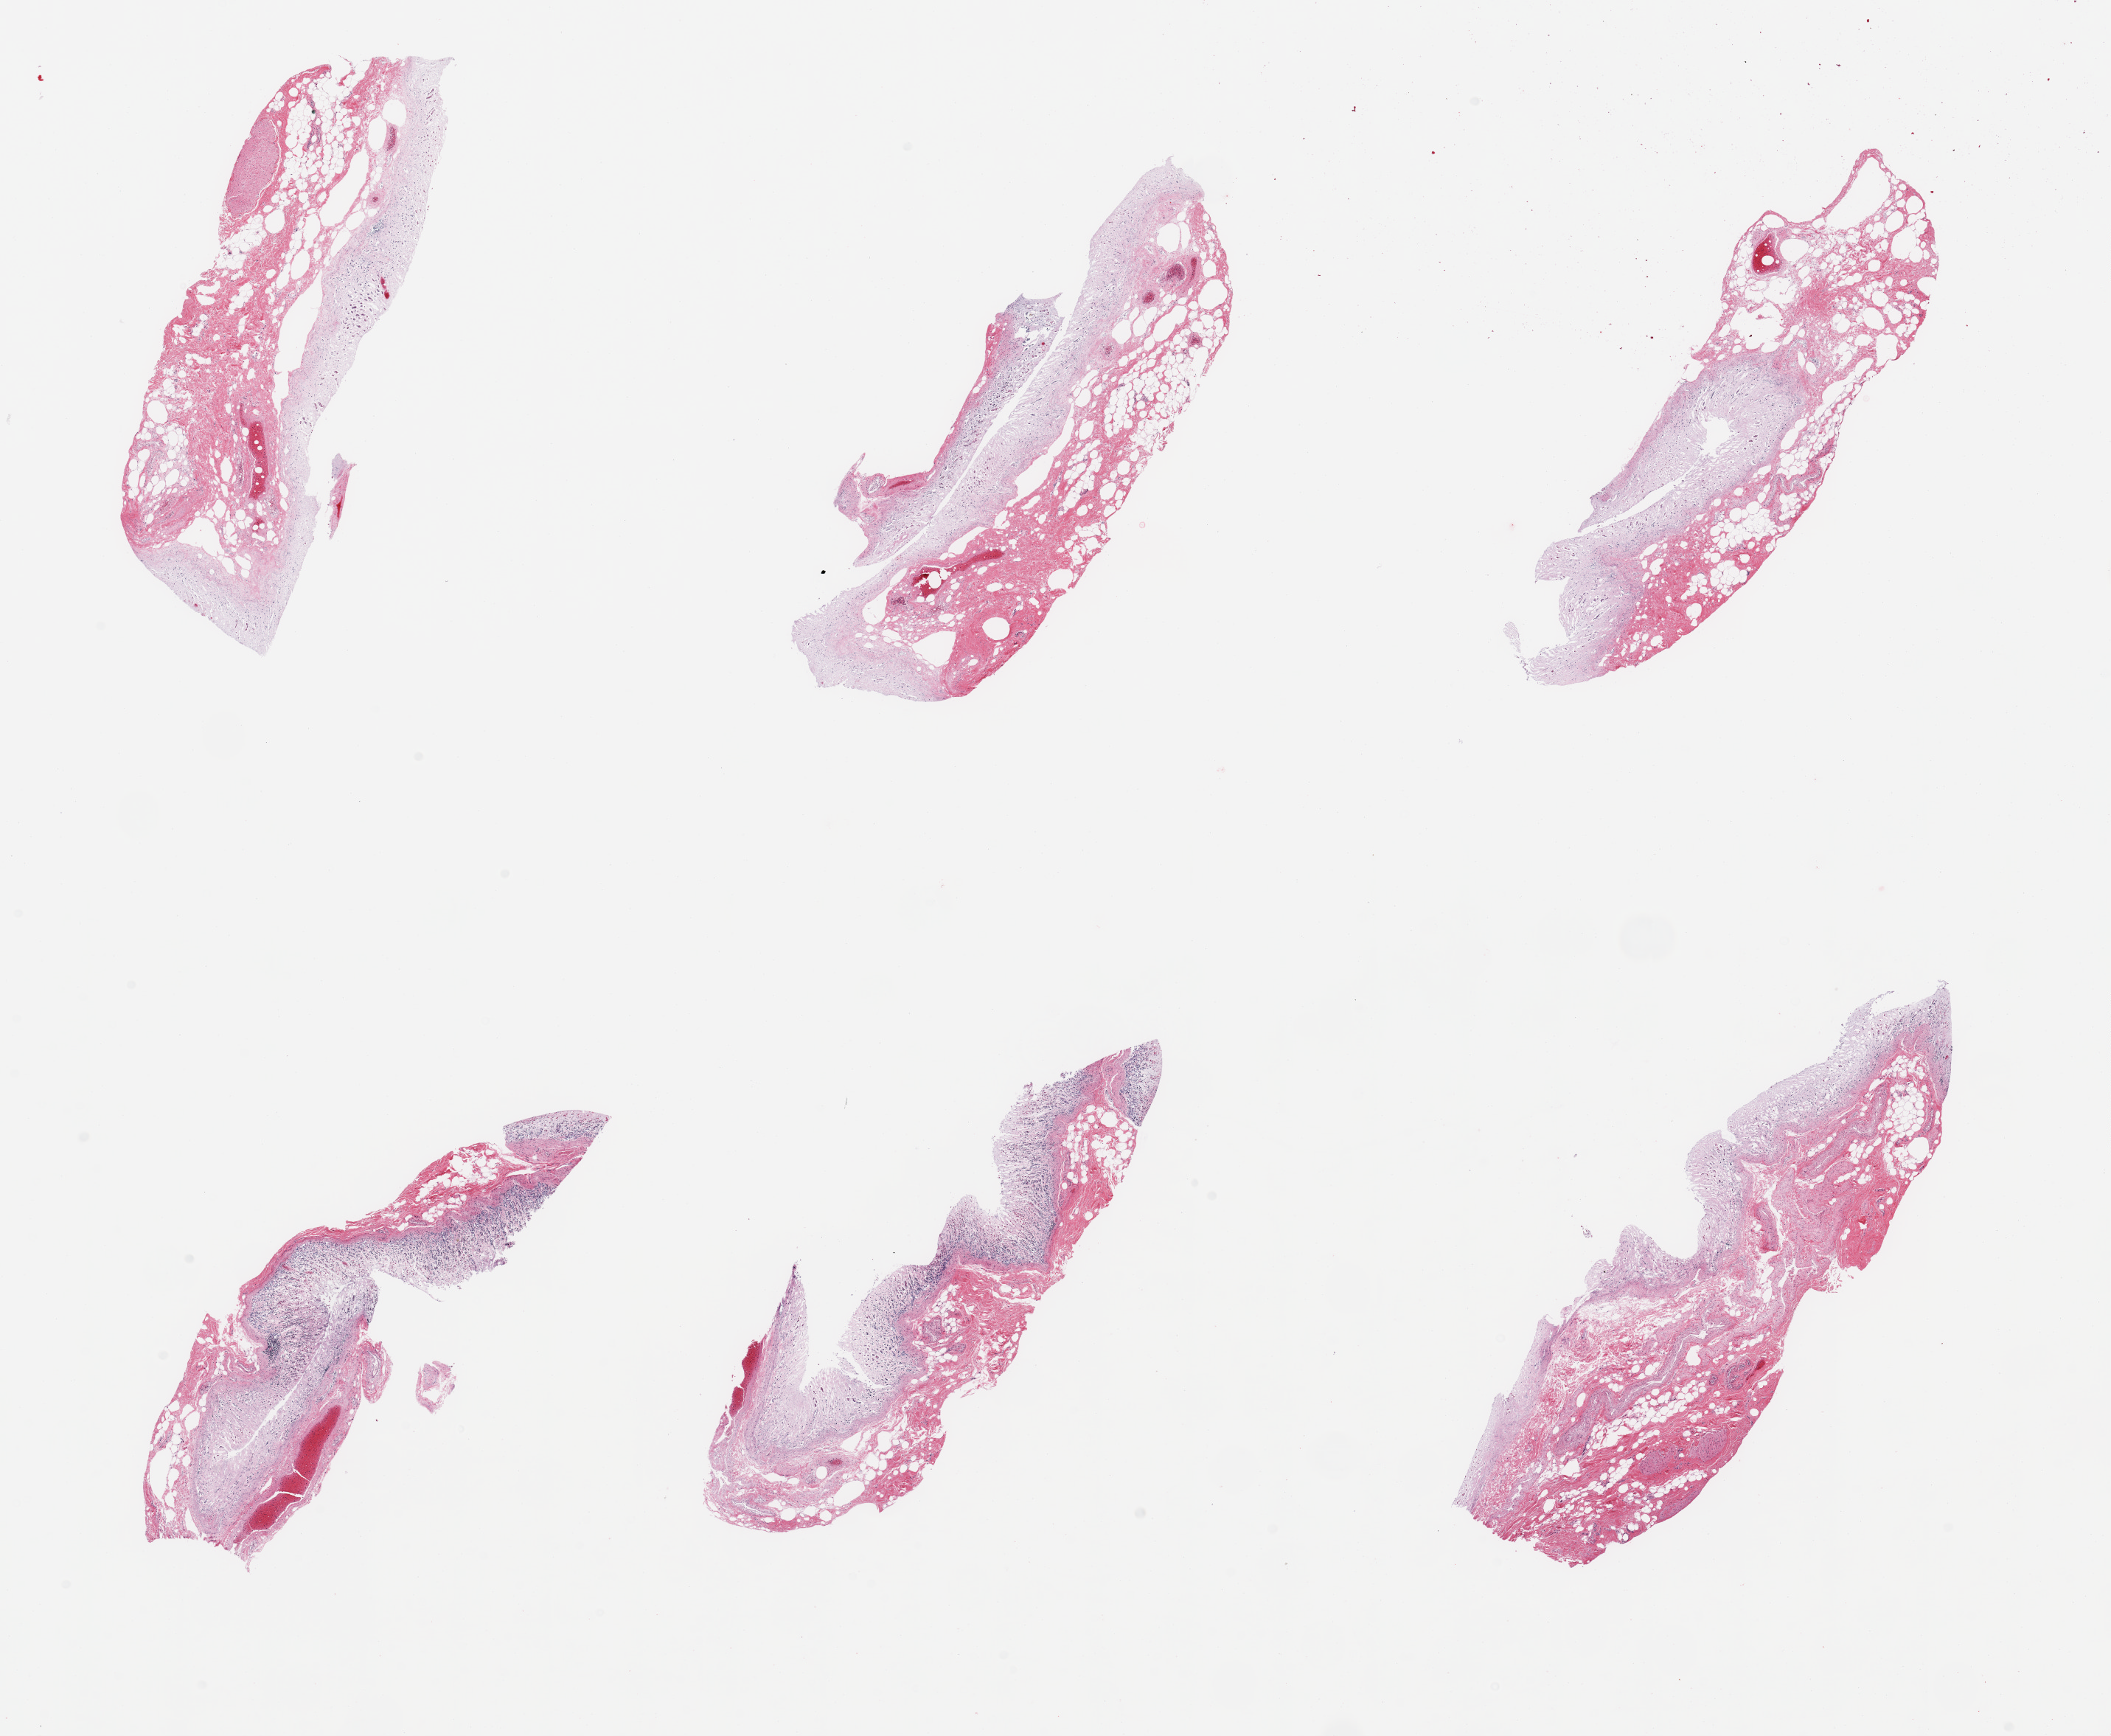
Hematoxylin and eosin (H&E) whole-slide image, brightfield, shown as a low-resolution overview of the whole scanned area (about 22.6 x 18.6 mm, acquisition: 20x scan), PAXgene-fixed paraffin-embedded (PFPE) section, target tissue: stomach, donor tissue sample. Donor: male.
* review note (as recorded): 6 pieces; tissue totally autolyzed